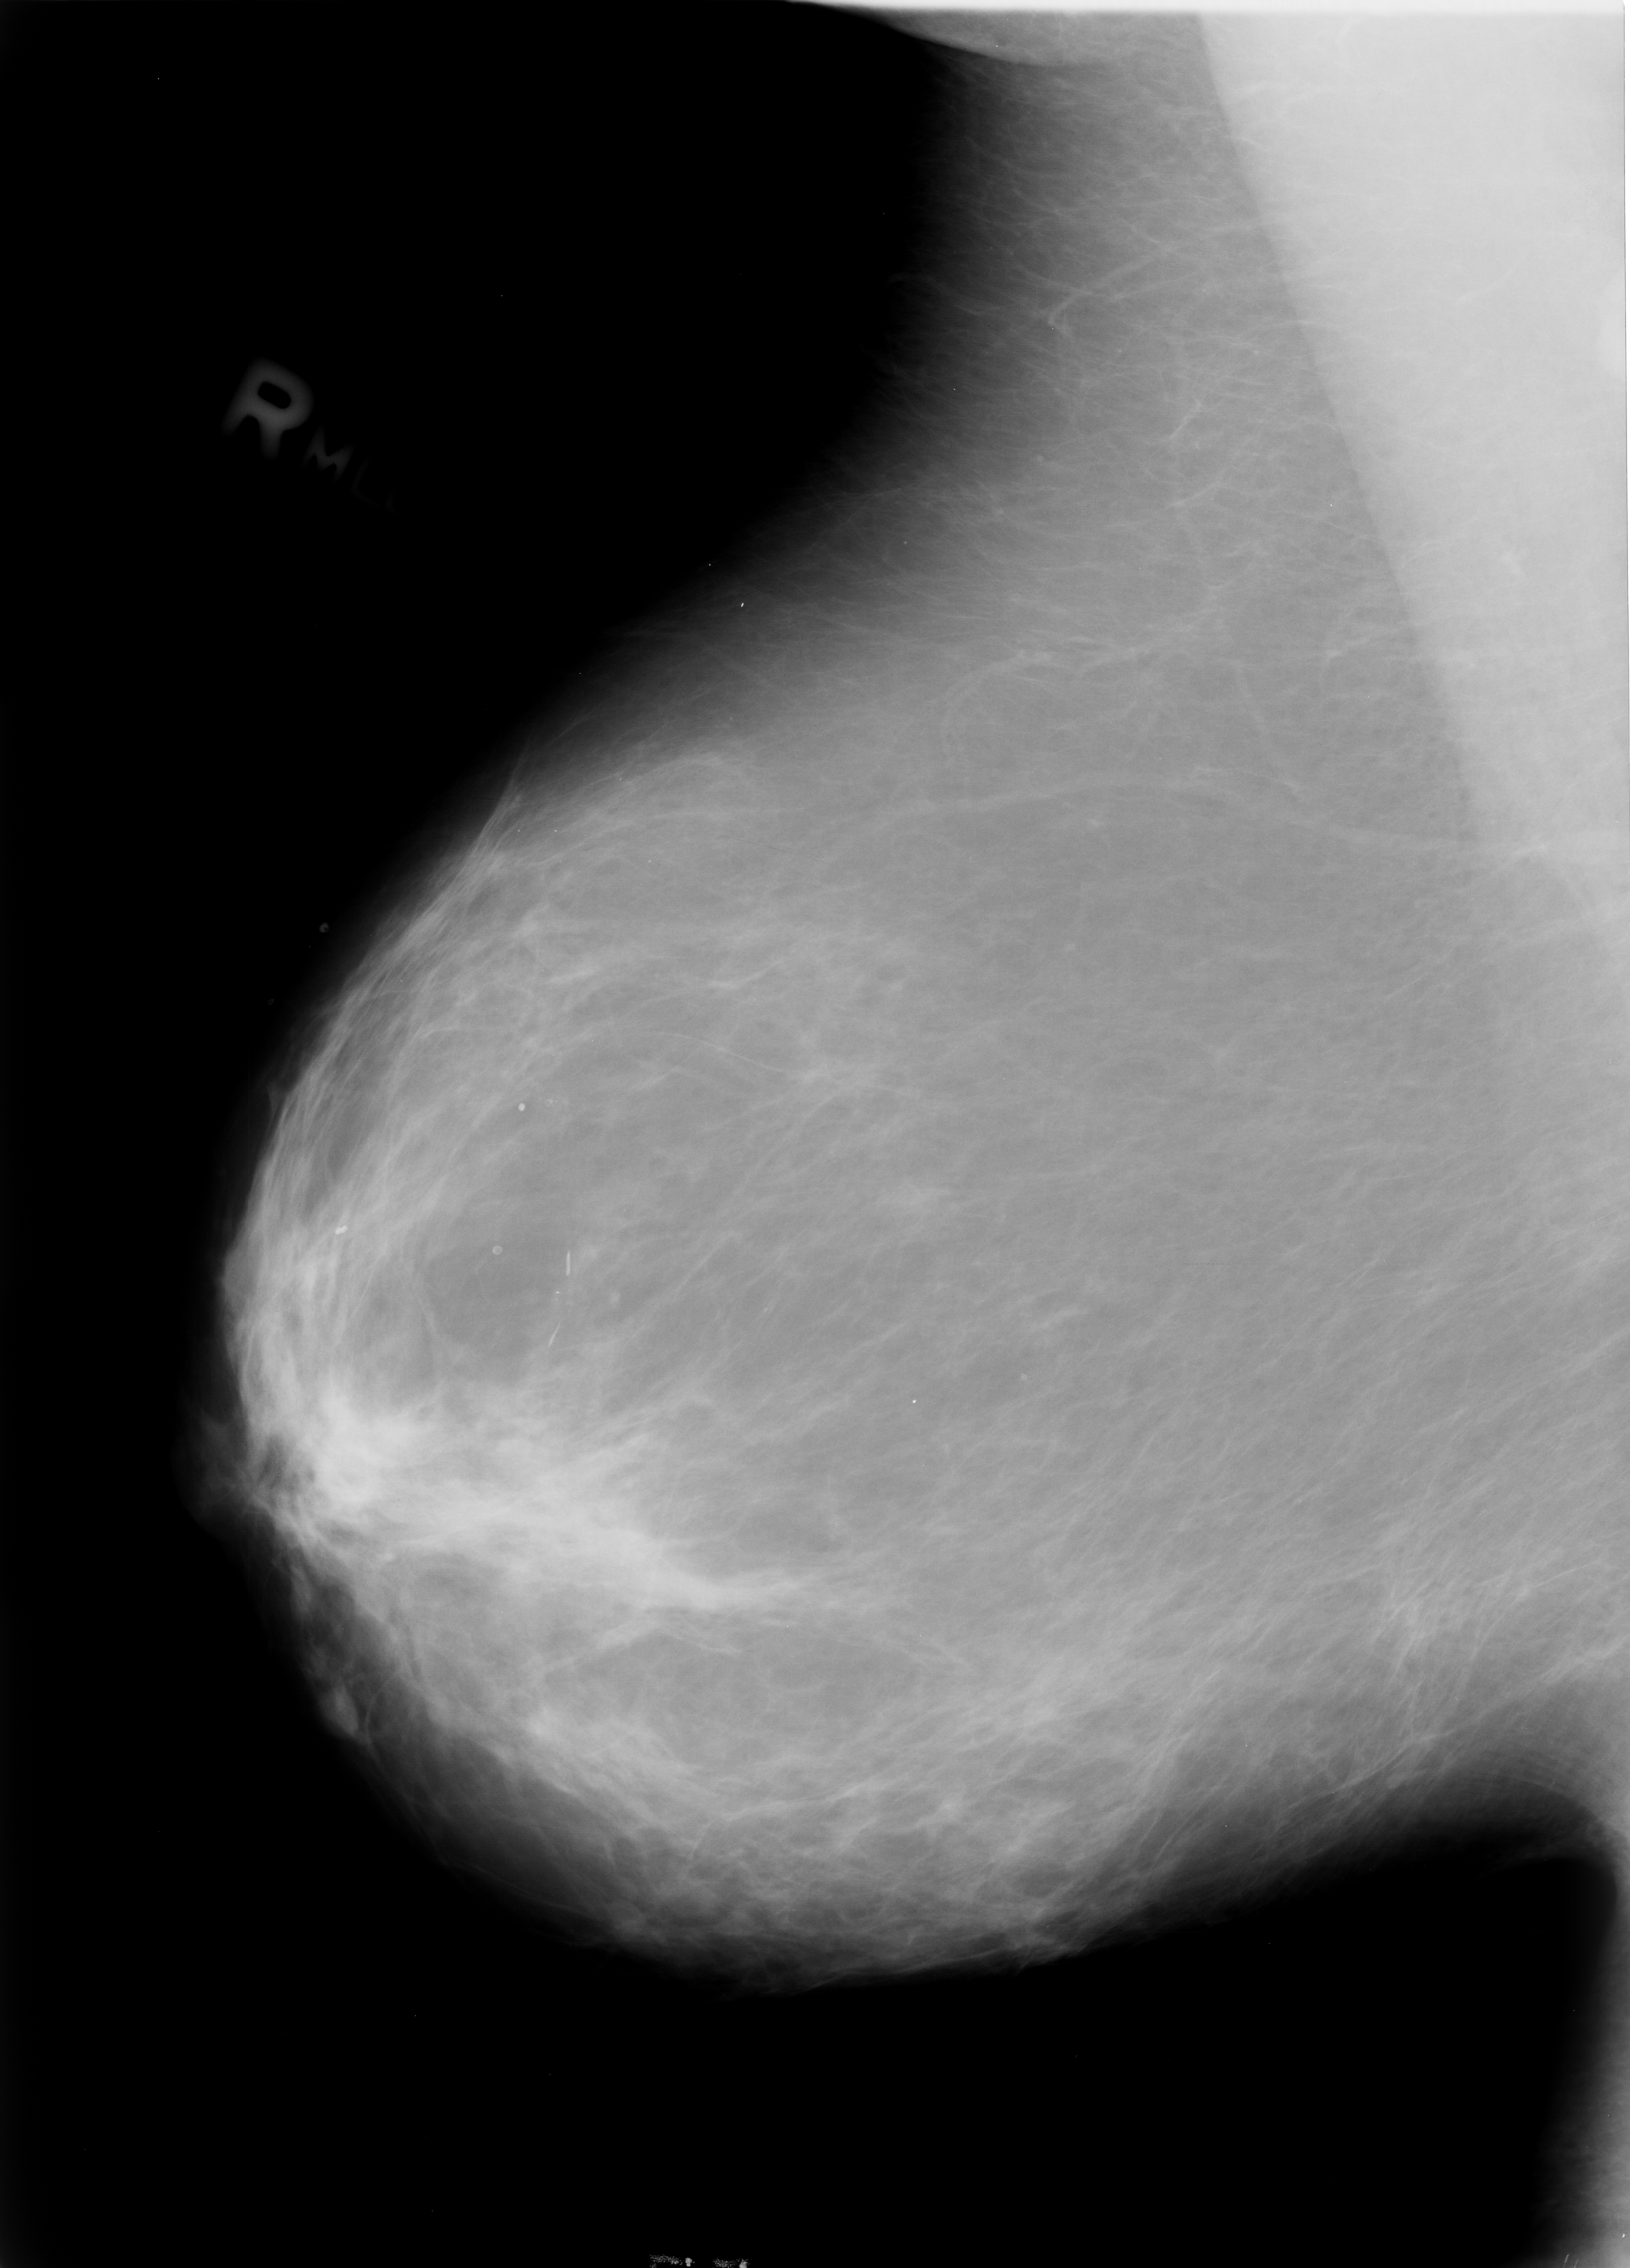
Mammogram (digitized film); right breast; MLO view; BI-RADS breast density category 2 (scale 1–4); 1630 × 2268 image matrix.
Expert-marked regions of interest on this film, with their recorded descriptors:
- calcifications, morphology amorphous / pleomorphic, distribution clustered; BI-RADS assessment category 4; pathology result (as recorded, not read from the image): benign: box from (x=511, y=1067) to (x=579, y=1141) px